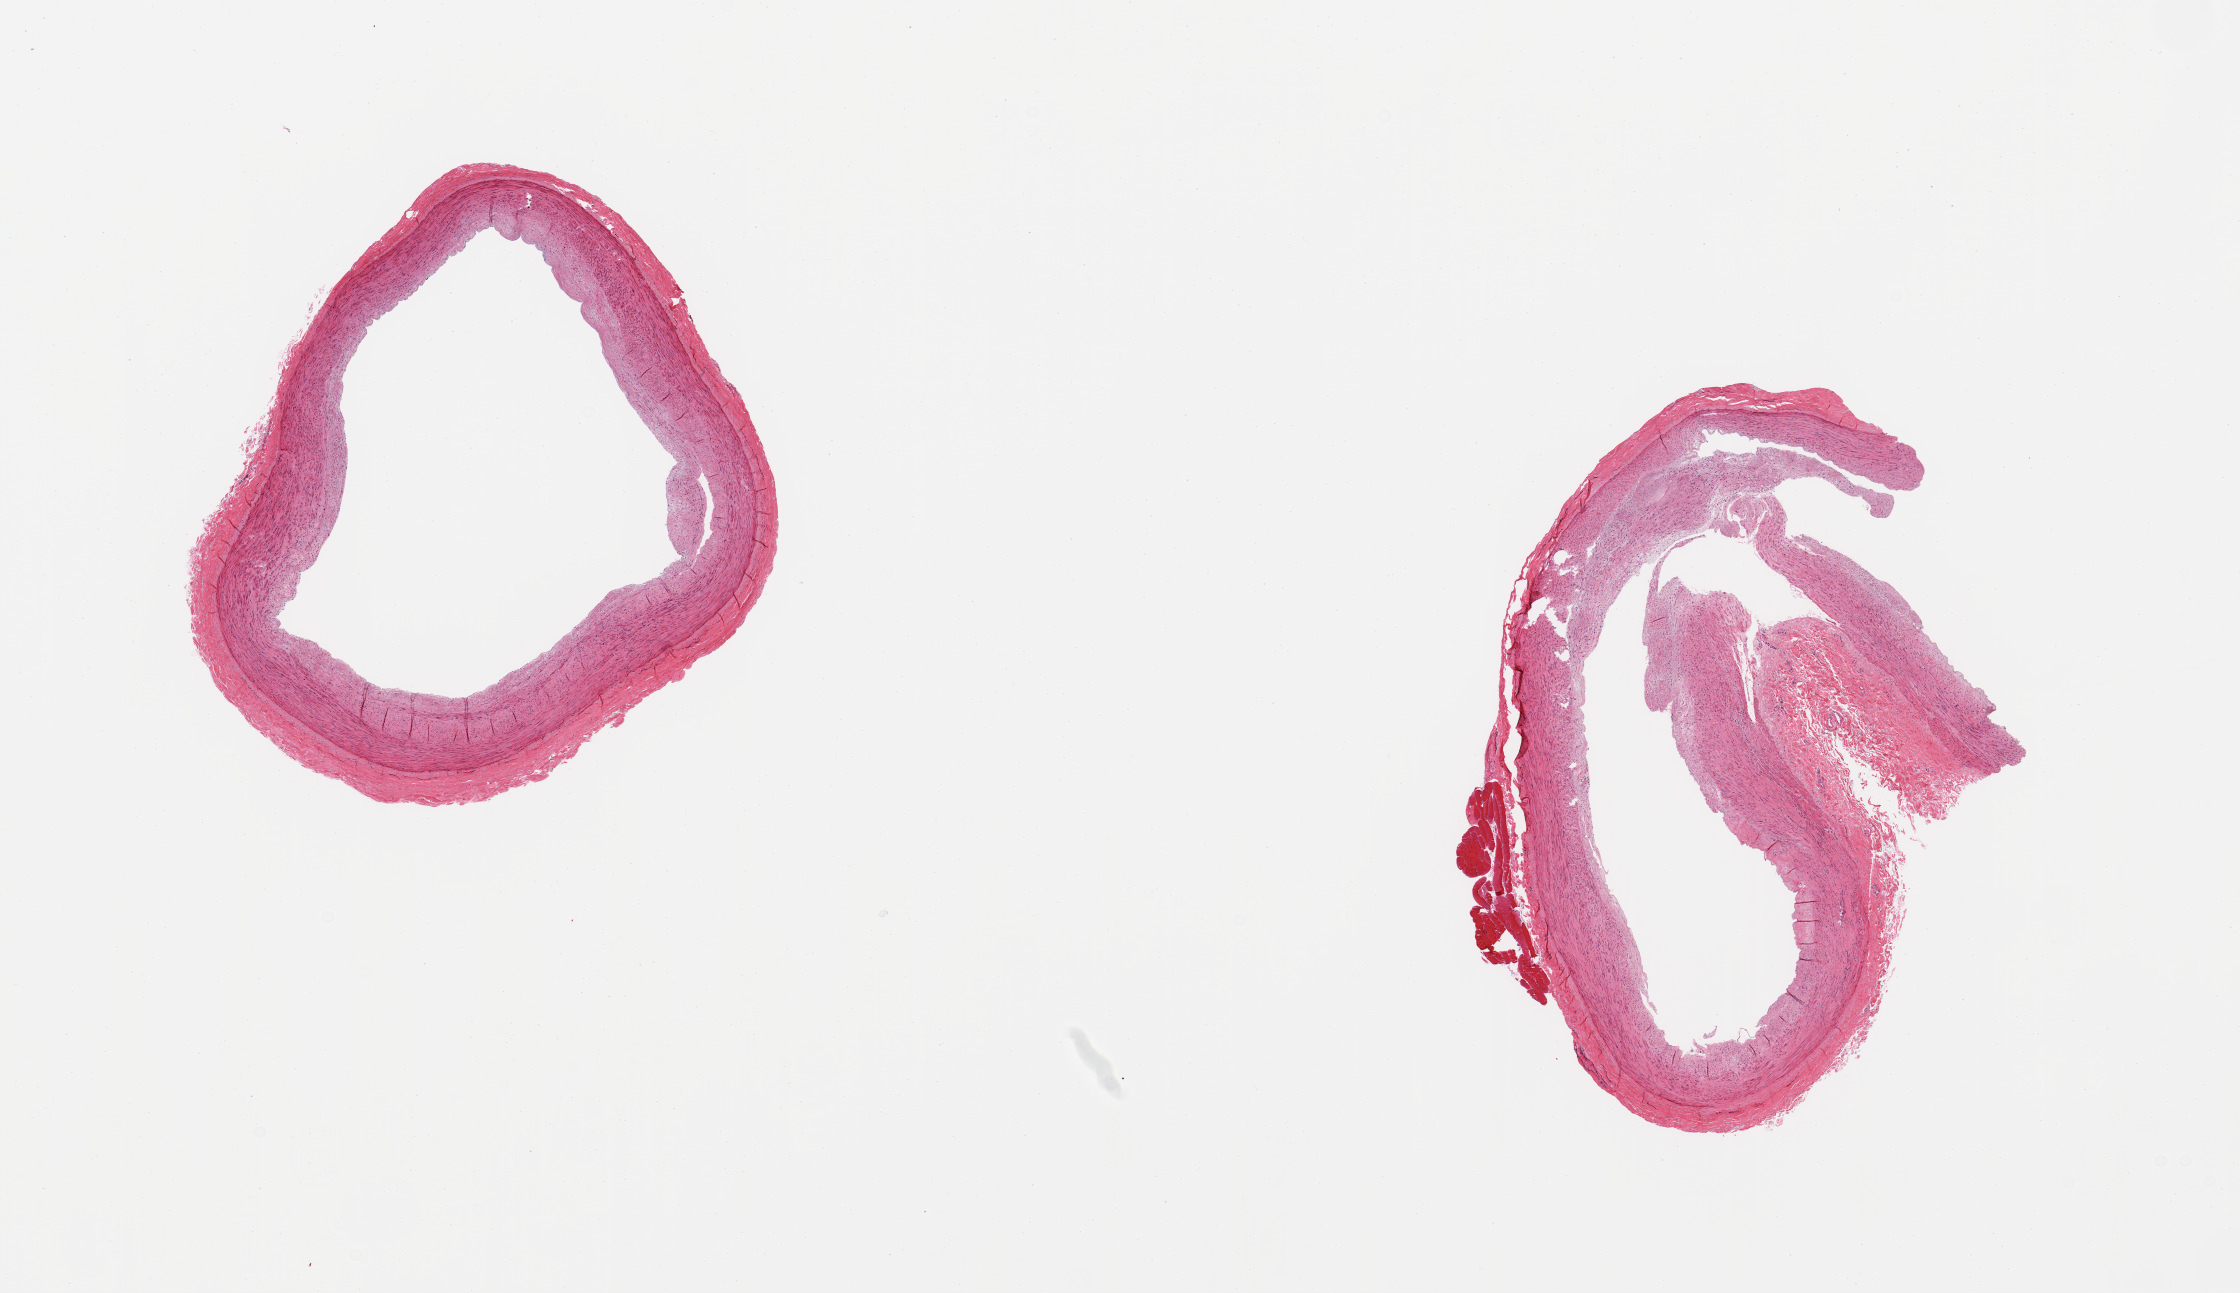
Whole-slide image, haematoxylin and eosin stain, a low-resolution overview of the entire scanned area, about 17.7 x 10.2 mm. PAXgene-fixed paraffin-embedded (PFPE) section. Target tissue: tibial artery. Donor tissue sample. Donor: male.
Review note (as recorded): 2 pieces, no adherent fat; minimal atherosis.